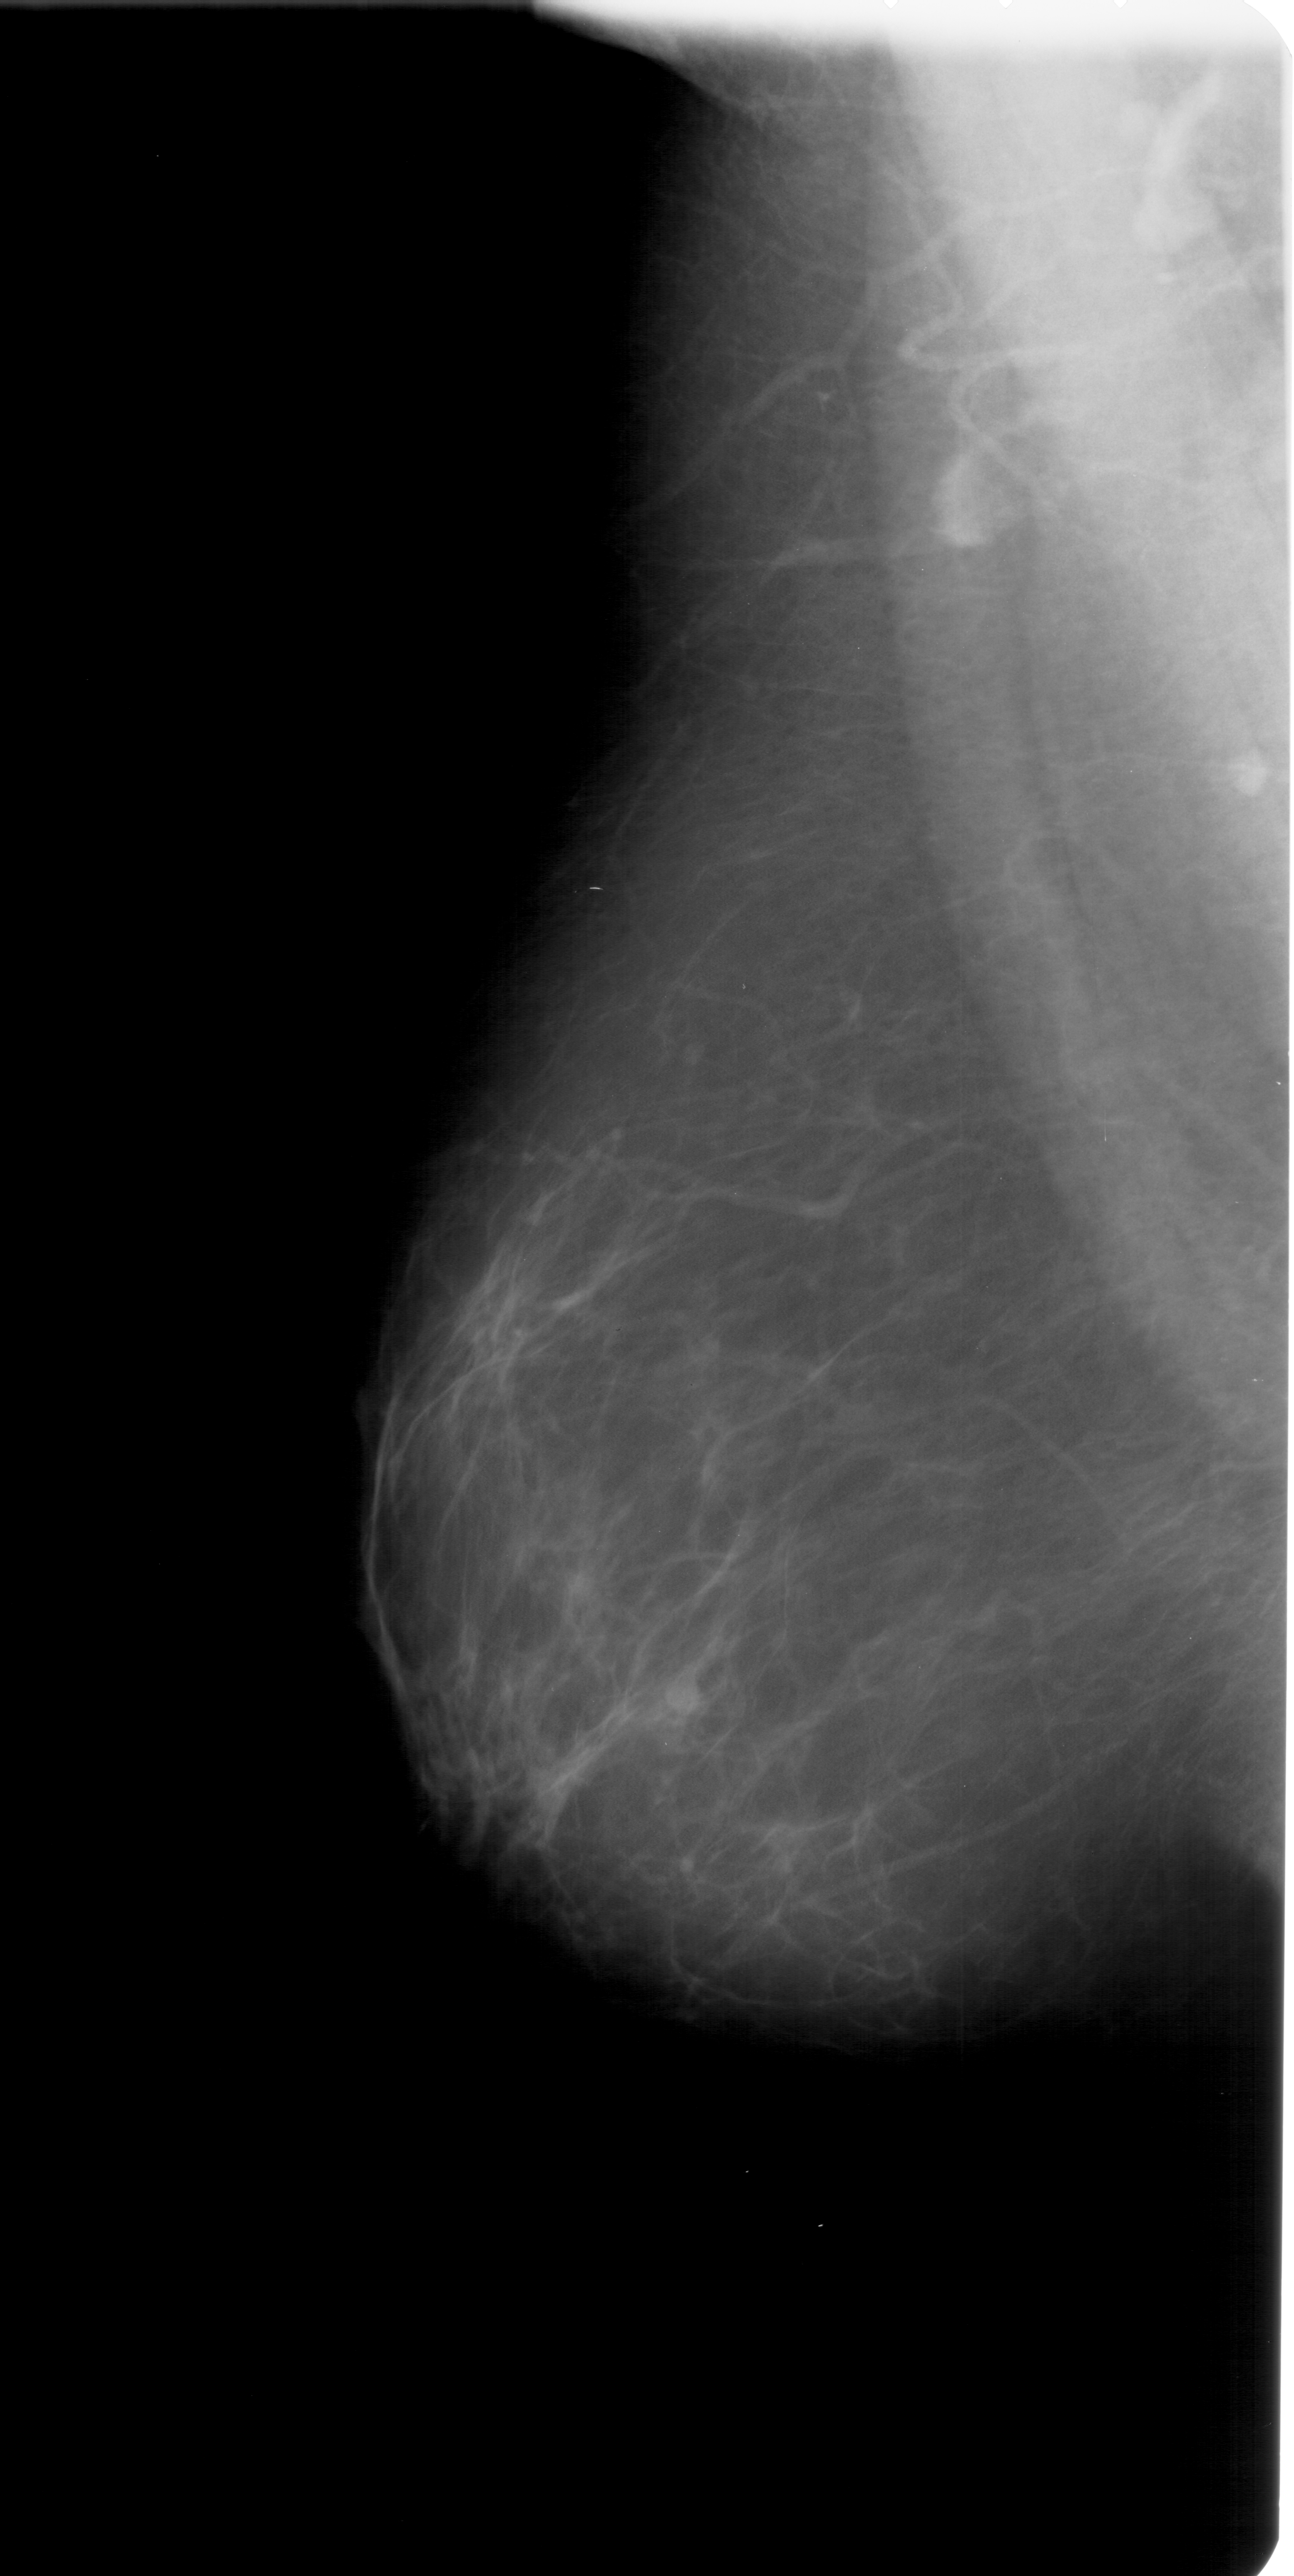
Mammogram (digitized film), left breast, mediolateral oblique (MLO) view, BI-RADS breast density category 2 (scale 1–4).
Marked abnormality: mass, shape lobulated, margins ill defined; BI-RADS assessment category 4; subtlety rating 3 on a 1 (subtle) to 5 (obvious) scale; pathology result (as recorded, not read from the image): benign.